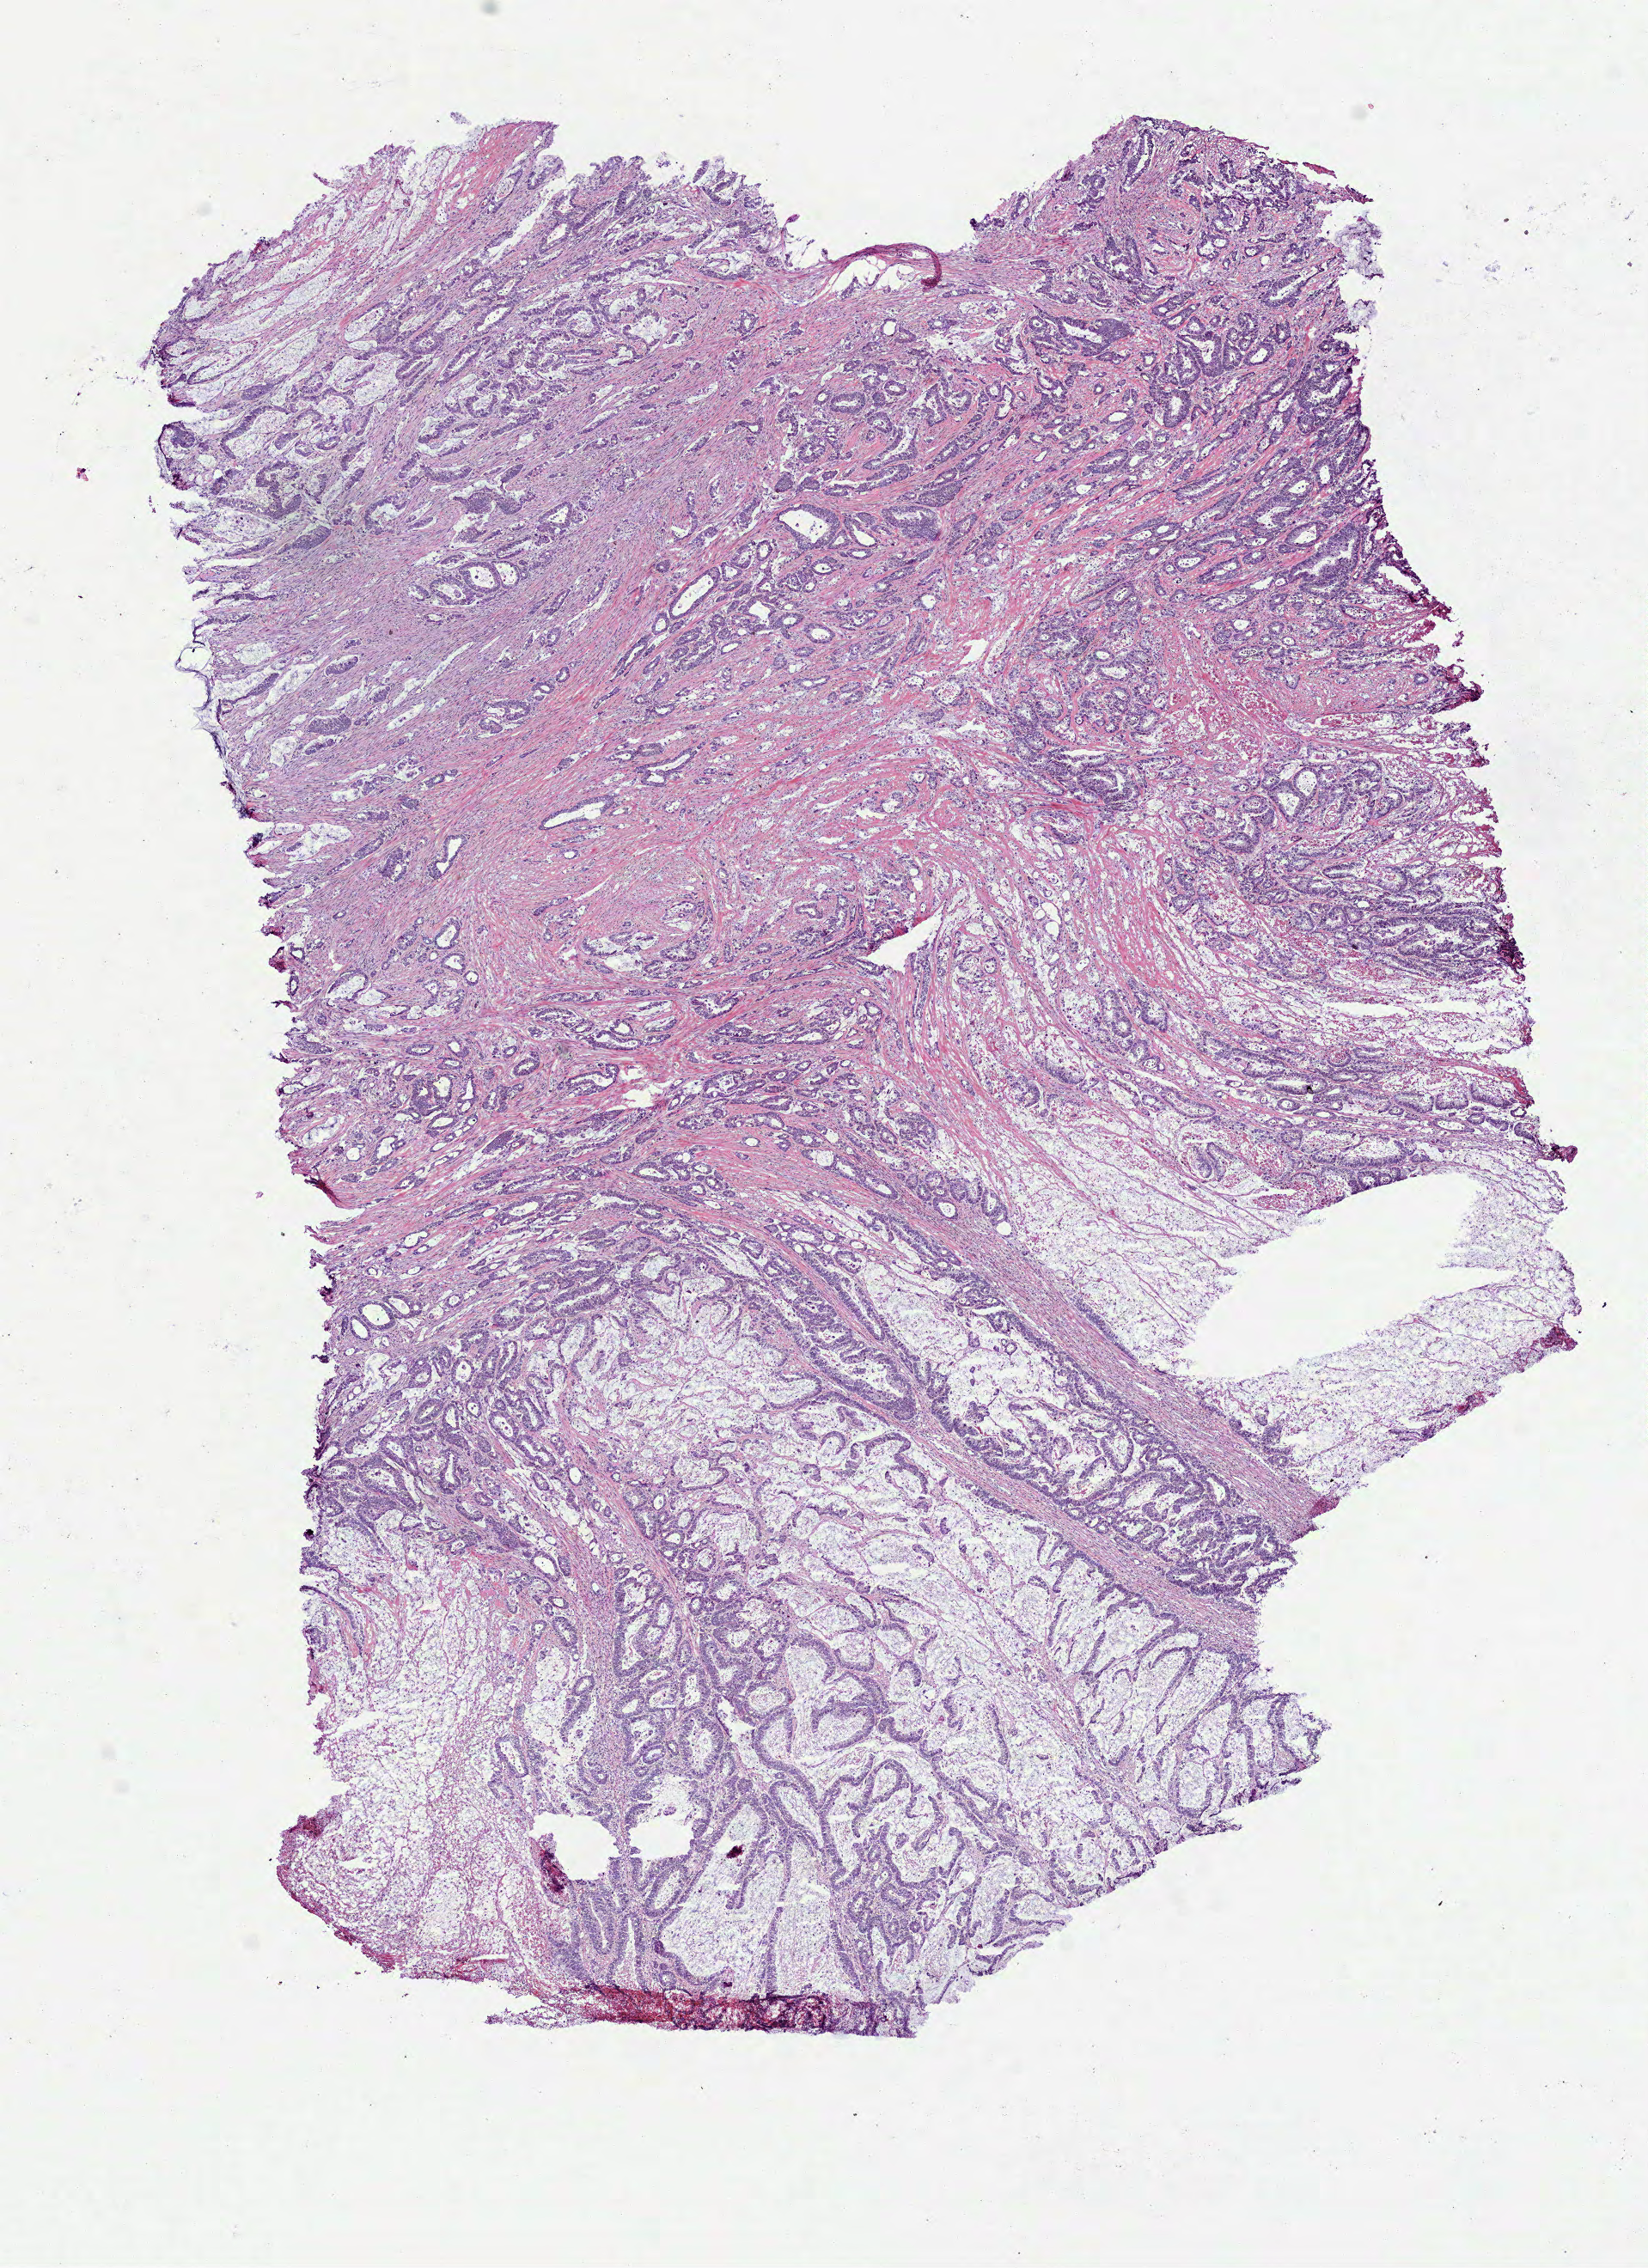
Whole-slide histology image, H&E-stained, shown as a low-resolution overview of the whole scanned area (about 7.7 x 10.6 mm, slide scanned at 40x); frozen section from the bottom of the tissue portion; primary tumour sample from the colon. Patient: male, age at initial diagnosis 73 years. Slide review estimates, as recorded: tumour cells 95%, tumour nuclei 80%, normal cells 0%, stromal cells 0%, necrosis 5%. Infiltration values recorded for this section: lymphocyte infiltration 5%, monocyte infiltration 5%, neutrophil infiltration 2%.
Pathologic diagnosis: Adenocarcinoma, NOS. Lymph nodes positive (case pathology): 0 of 14 examined. AJCC pathologic stage: IIA. TNM: T3 N0 M0.